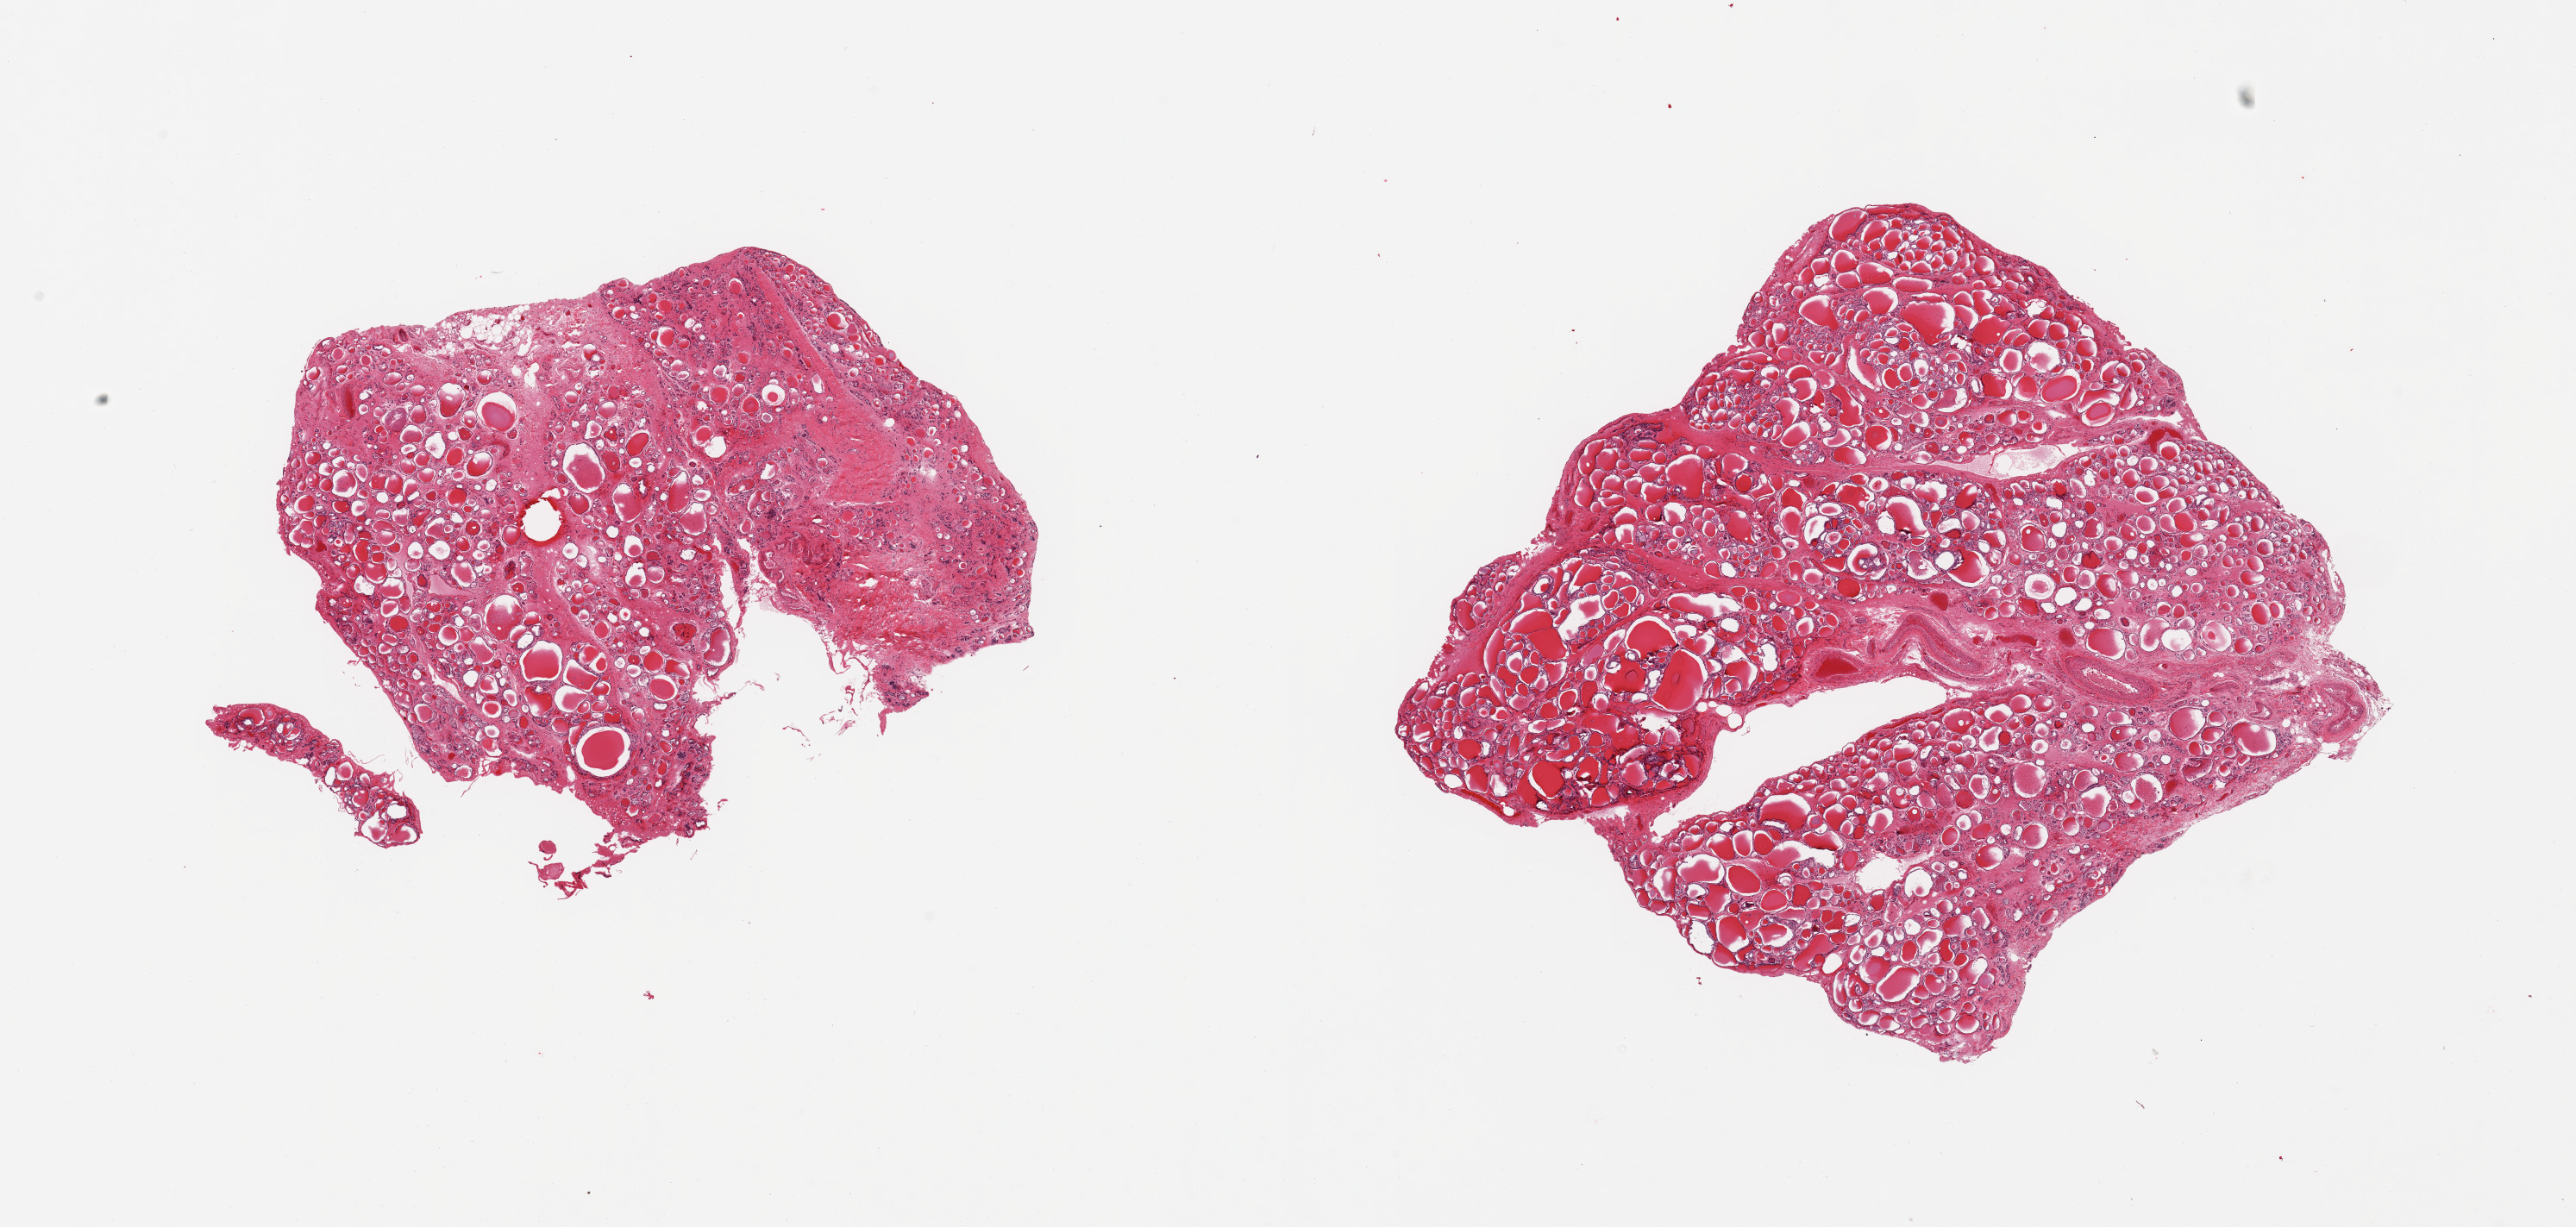
Haematoxylin and eosin whole-slide image, brightfield — shown as a low-resolution overview of the whole scanned area (about 23.6 x 11.3 mm, acquisition: 20x scan); PAXgene-fixed, paraffin-embedded tissue; section of thyroid (target tissue); tissue donor sample. Donor sex: female.
* pathologist's review note for this sample: 2 pieces; 20% fibrous content in 1 piece